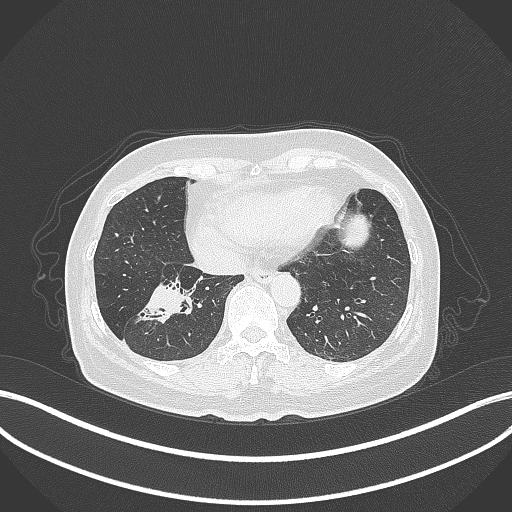
Chest CT, one axial slice. Slice 117 of 429 in the series (ordered by position). Reconstruction kernel B70f. 120 kVp. Lung window (W 1500 / L -600 HU). 1 mm slice thickness. 512 × 512 image matrix, field of view 400 × 400 mm. Female patient, age 67 years. Case-level facts recorded for this patient, not image findings: clinical TNM (as recorded): T1c N1 M0.
Structures marked on this image (bounding box drawn by a radiologist):
- lung tumour (recorded histology: adenocarcinoma): box from (x=128, y=272) to (x=190, y=329) px